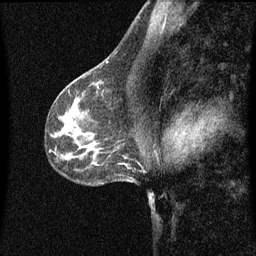
Breast MRI (dynamic contrast-enhanced), one sagittal slice; position 38 of 60 along the scan axis; dynamic contrast-enhanced series, image 2 of 3 at this slice position (ordered by acquisition); 1.5 T; TE 4.2 ms, TR 8.4 ms; 2 mm slice thickness; 256 × 256 image matrix, field of view 200 × 200 mm. Patient: female, 41 years.
Annotated regions visible in this slice (semi-automatically segmented with operator editing):
- analysis volume of interest (the breast-tissue region the enhancement analysis was run in; not a lesion): bounding box <94,72,113,97> (left, top, right, bottom; pixels)
- tumour enhancement mask (voxels above the 70 % enhancement threshold inside the analysis volume of interest): <96,82,101,89>